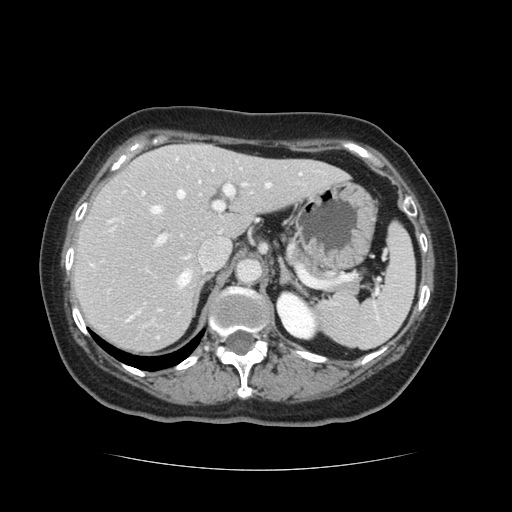
Contrast-enhanced abdominal CT, one axial slice; position 83 of 128 along the scan axis; 120 kVp; intravenous contrast given; soft-tissue window (W 400 / L 40 HU); 2.5 mm slice thickness; 512 × 512 image matrix. Female patient, age 67 years. Case-level facts recorded for this patient, not image findings: diagnosis: colorectal cancer liver metastases, imaged before liver resection; multiple liver metastases: yes; largest metastasis: 3 cm; disease in both lobes: yes.
Structures marked on this image (outlined manually by an expert reader):
- hepatic veins: bounding box [x1, y1, x2, y2] px = [132, 184, 271, 318]
- liver: [74, 145, 344, 353]
- planned liver remnant (the part of the liver to remain after resection): [74, 157, 344, 353]
- portal vein (with intrahepatic branches): [144, 160, 248, 243]